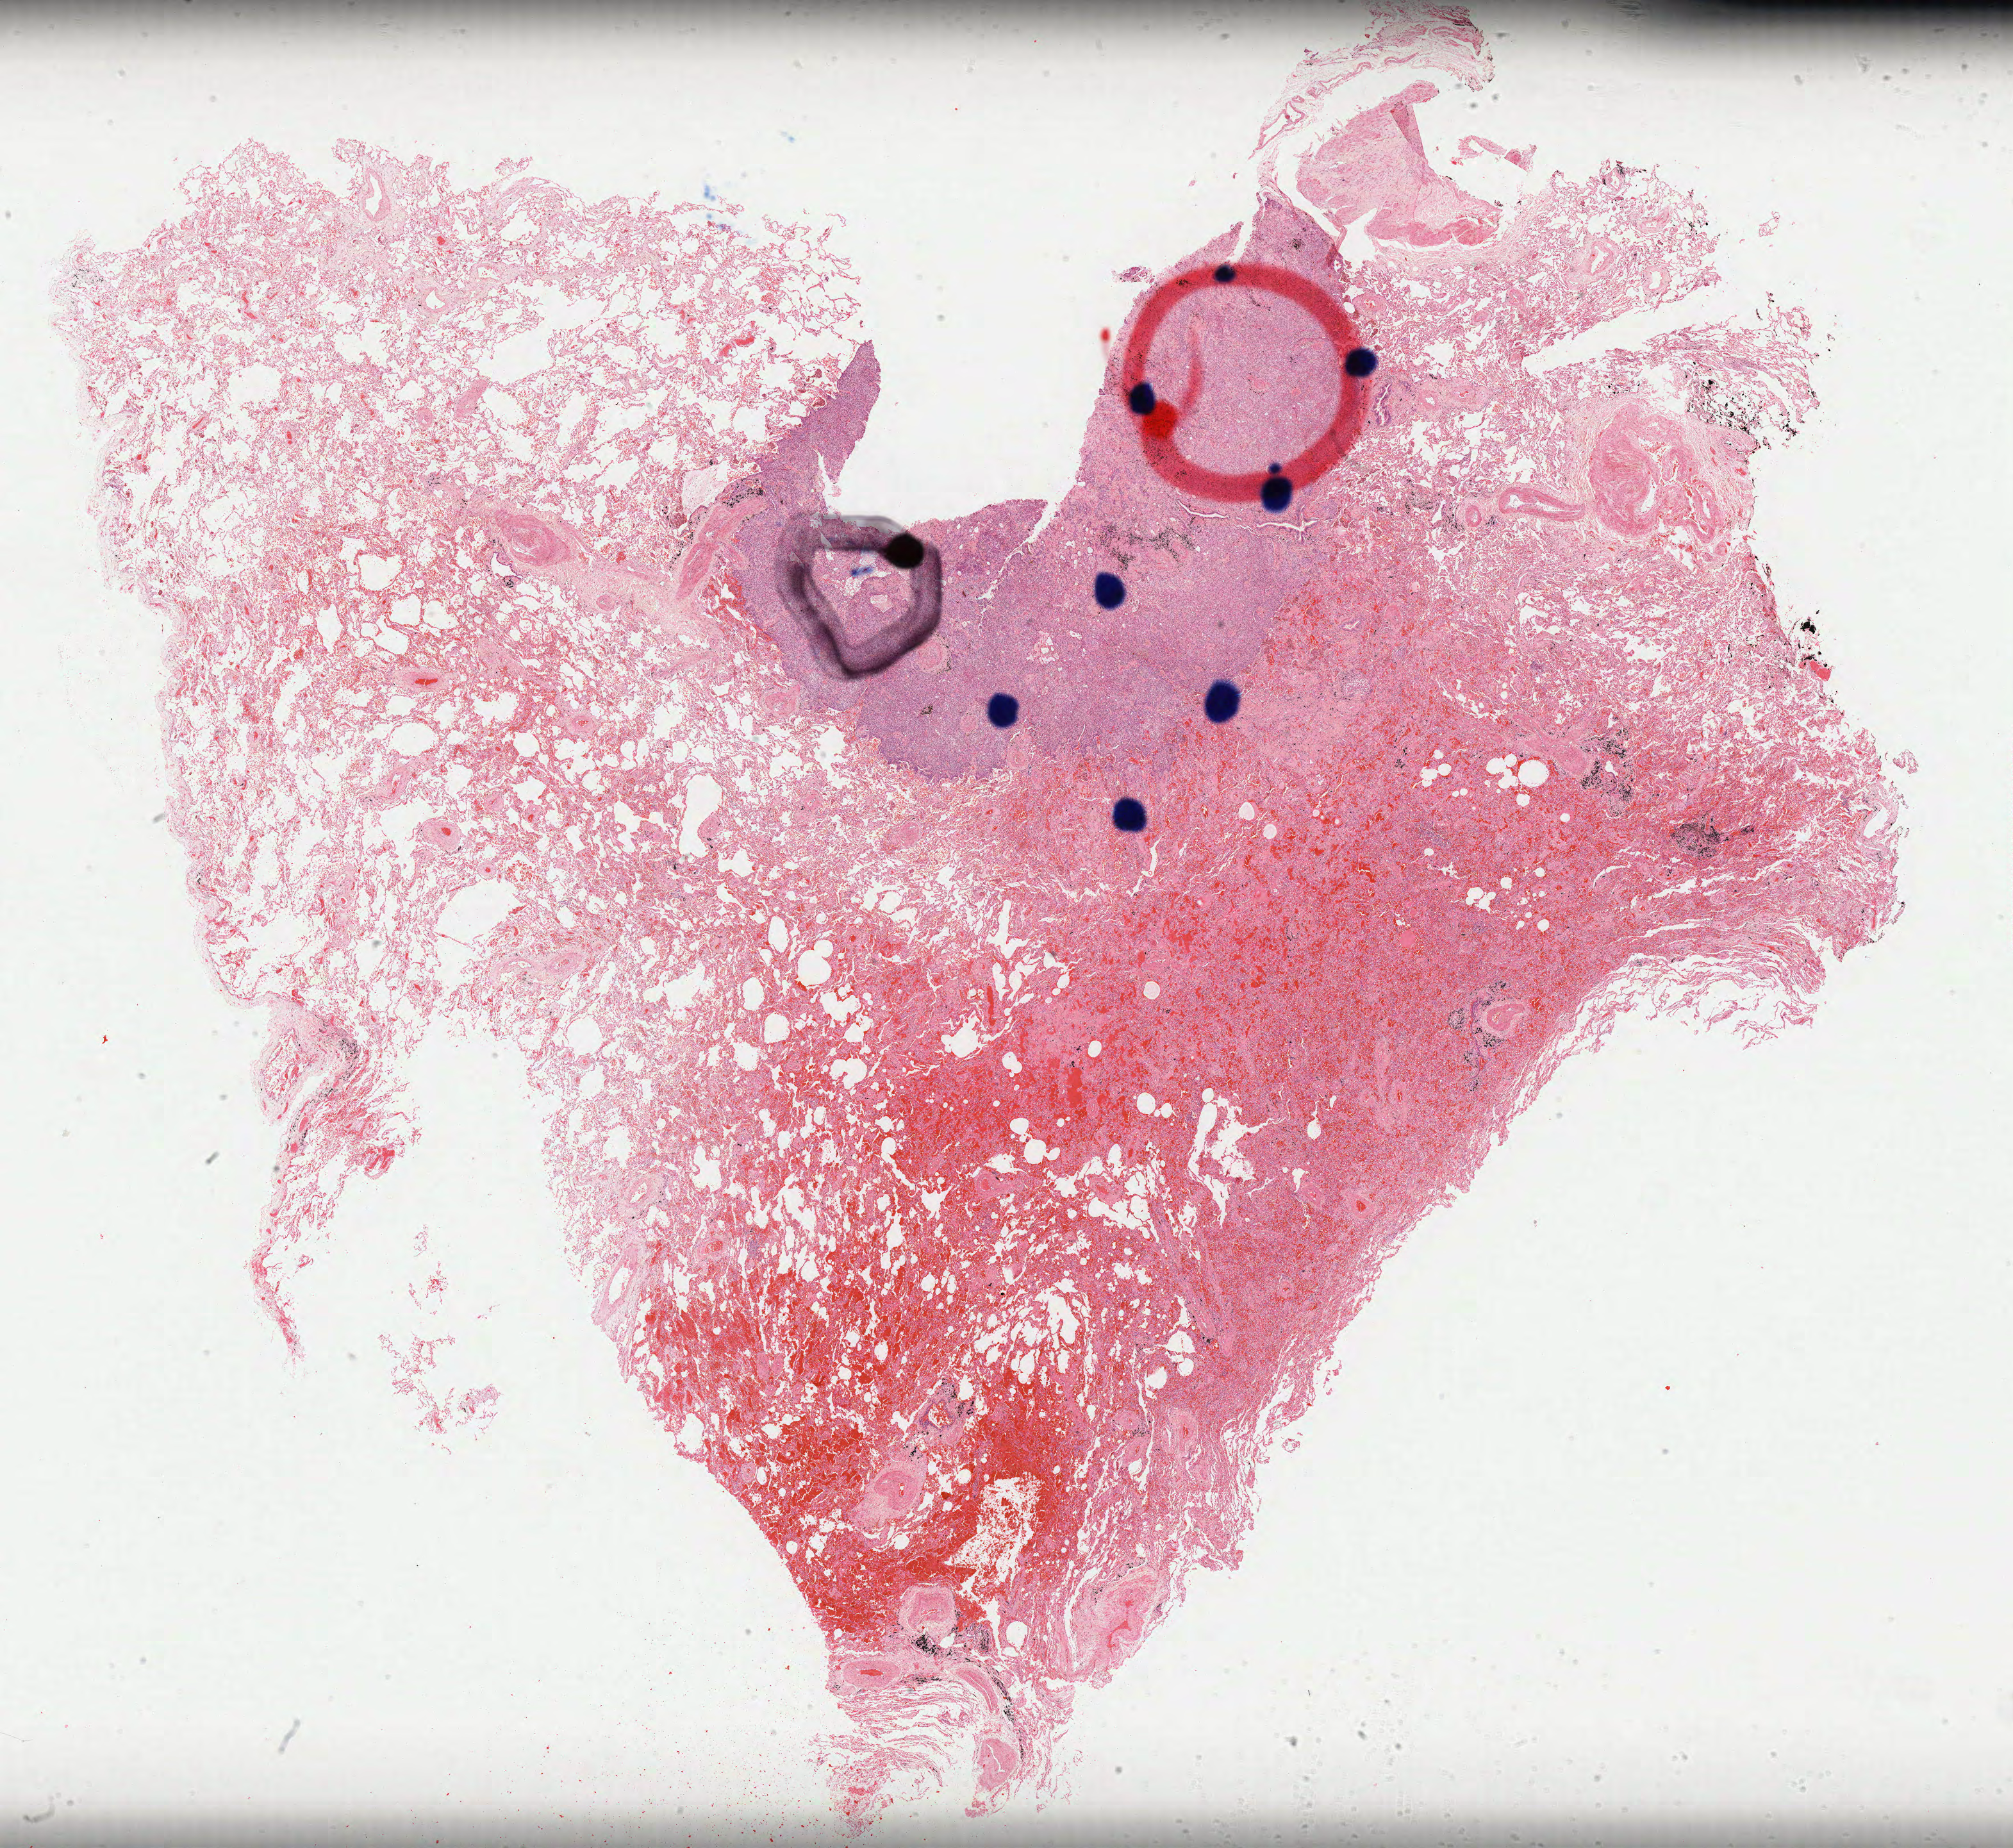
Hematoxylin and eosin (H&E) stained whole-slide image — low-resolution overview of the scanned area, about 25.3 x 23.2 mm. FFPE section. Sample: primary tumour, lung. Patient: male, age at initial diagnosis 74 years.
• diagnosis: Basaloid squamous cell carcinoma (upper lobe, lung)
• AJCC pathologic stage: IA